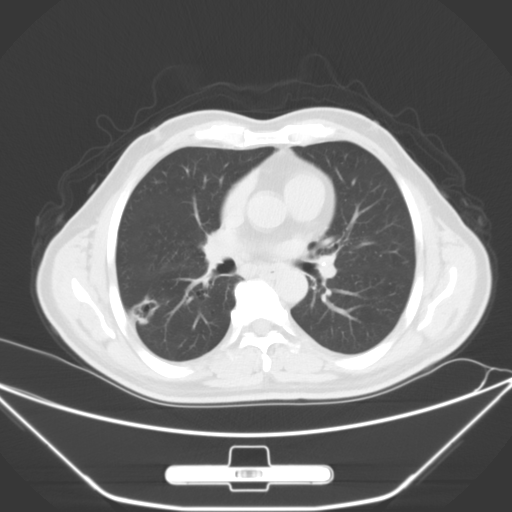
Chest CT, one axial slice; 120 kVp; lung window (W 1500 / L -600 HU); 5 mm slice thickness; 512 × 512 image matrix, field of view 398 × 398 mm. Patient: male, 71 years. From the clinical record (not read from this slice): clinical TNM (as recorded): T1c N0 M0; histopathological grade: G2.
Annotated regions visible in this slice (rectangle marked by the reading radiologist):
- lung tumour (recorded histology: adenocarcinoma): bounding box (x1, y1, x2, y2) in pixels: (128, 295, 161, 330)